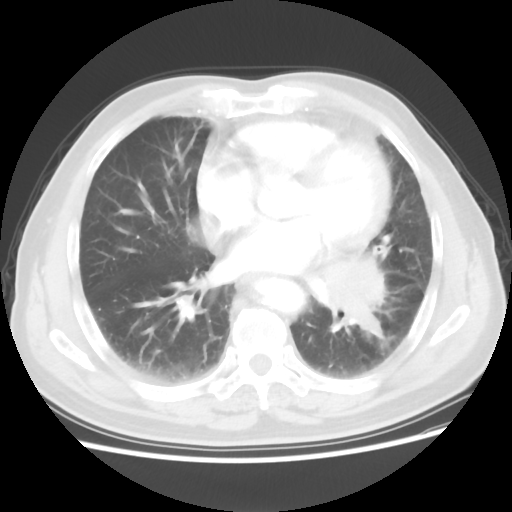
Chest CT, one axial slice. Position 26 of 56 along the scan axis. Reconstruction kernel STANDARD. 120 kVp. Lung window (W 1500 / L -600 HU). 512 × 512 image matrix, field of view 360 × 360 mm. Patient: male, 75 years. From the clinical record (not read from this slice): clinical TNM (as recorded): T3 N0 M0.
Annotated regions visible in this slice (rectangle marked by the reading radiologist):
- lung tumour (recorded histology: squamous cell carcinoma): box from (x=309, y=256) to (x=398, y=347) px